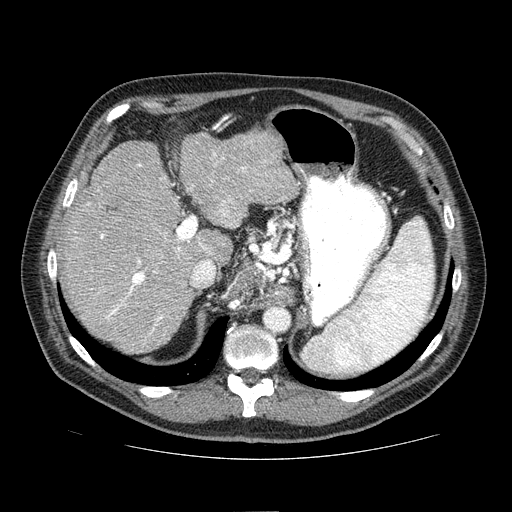
Contrast-enhanced abdominal CT (liver protocol), one axial slice; slice 50 of 81 in the series (ordered by position); one of 2 acquisitions stored at this slice position; soft-tissue window (W 400 / L 40 HU); 2.5 mm slice thickness; 512 × 512 image matrix, field of view 400 × 400 mm. From the clinical record (not read from this slice): diagnosis: hepatocellular carcinoma (patient treated with transarterial chemoembolisation; whether this scan precedes or follows treatment is not stated here); TNM stage (as recorded): Stage-IIIA; Child-Pugh class: A; tumour differentiation: well differentiated; tumour nodularity: multinodular.
Outlined on this slice (semi-automatically segmented with operator editing):
- liver parenchyma outside the tumour (the mass and vessels are separate outlines, so this box may not span the whole liver): bounding box [x1, y1, x2, y2] px = [60, 132, 299, 352]
- mass: [242, 130, 281, 167]
- liver vessels: [87, 151, 247, 335]